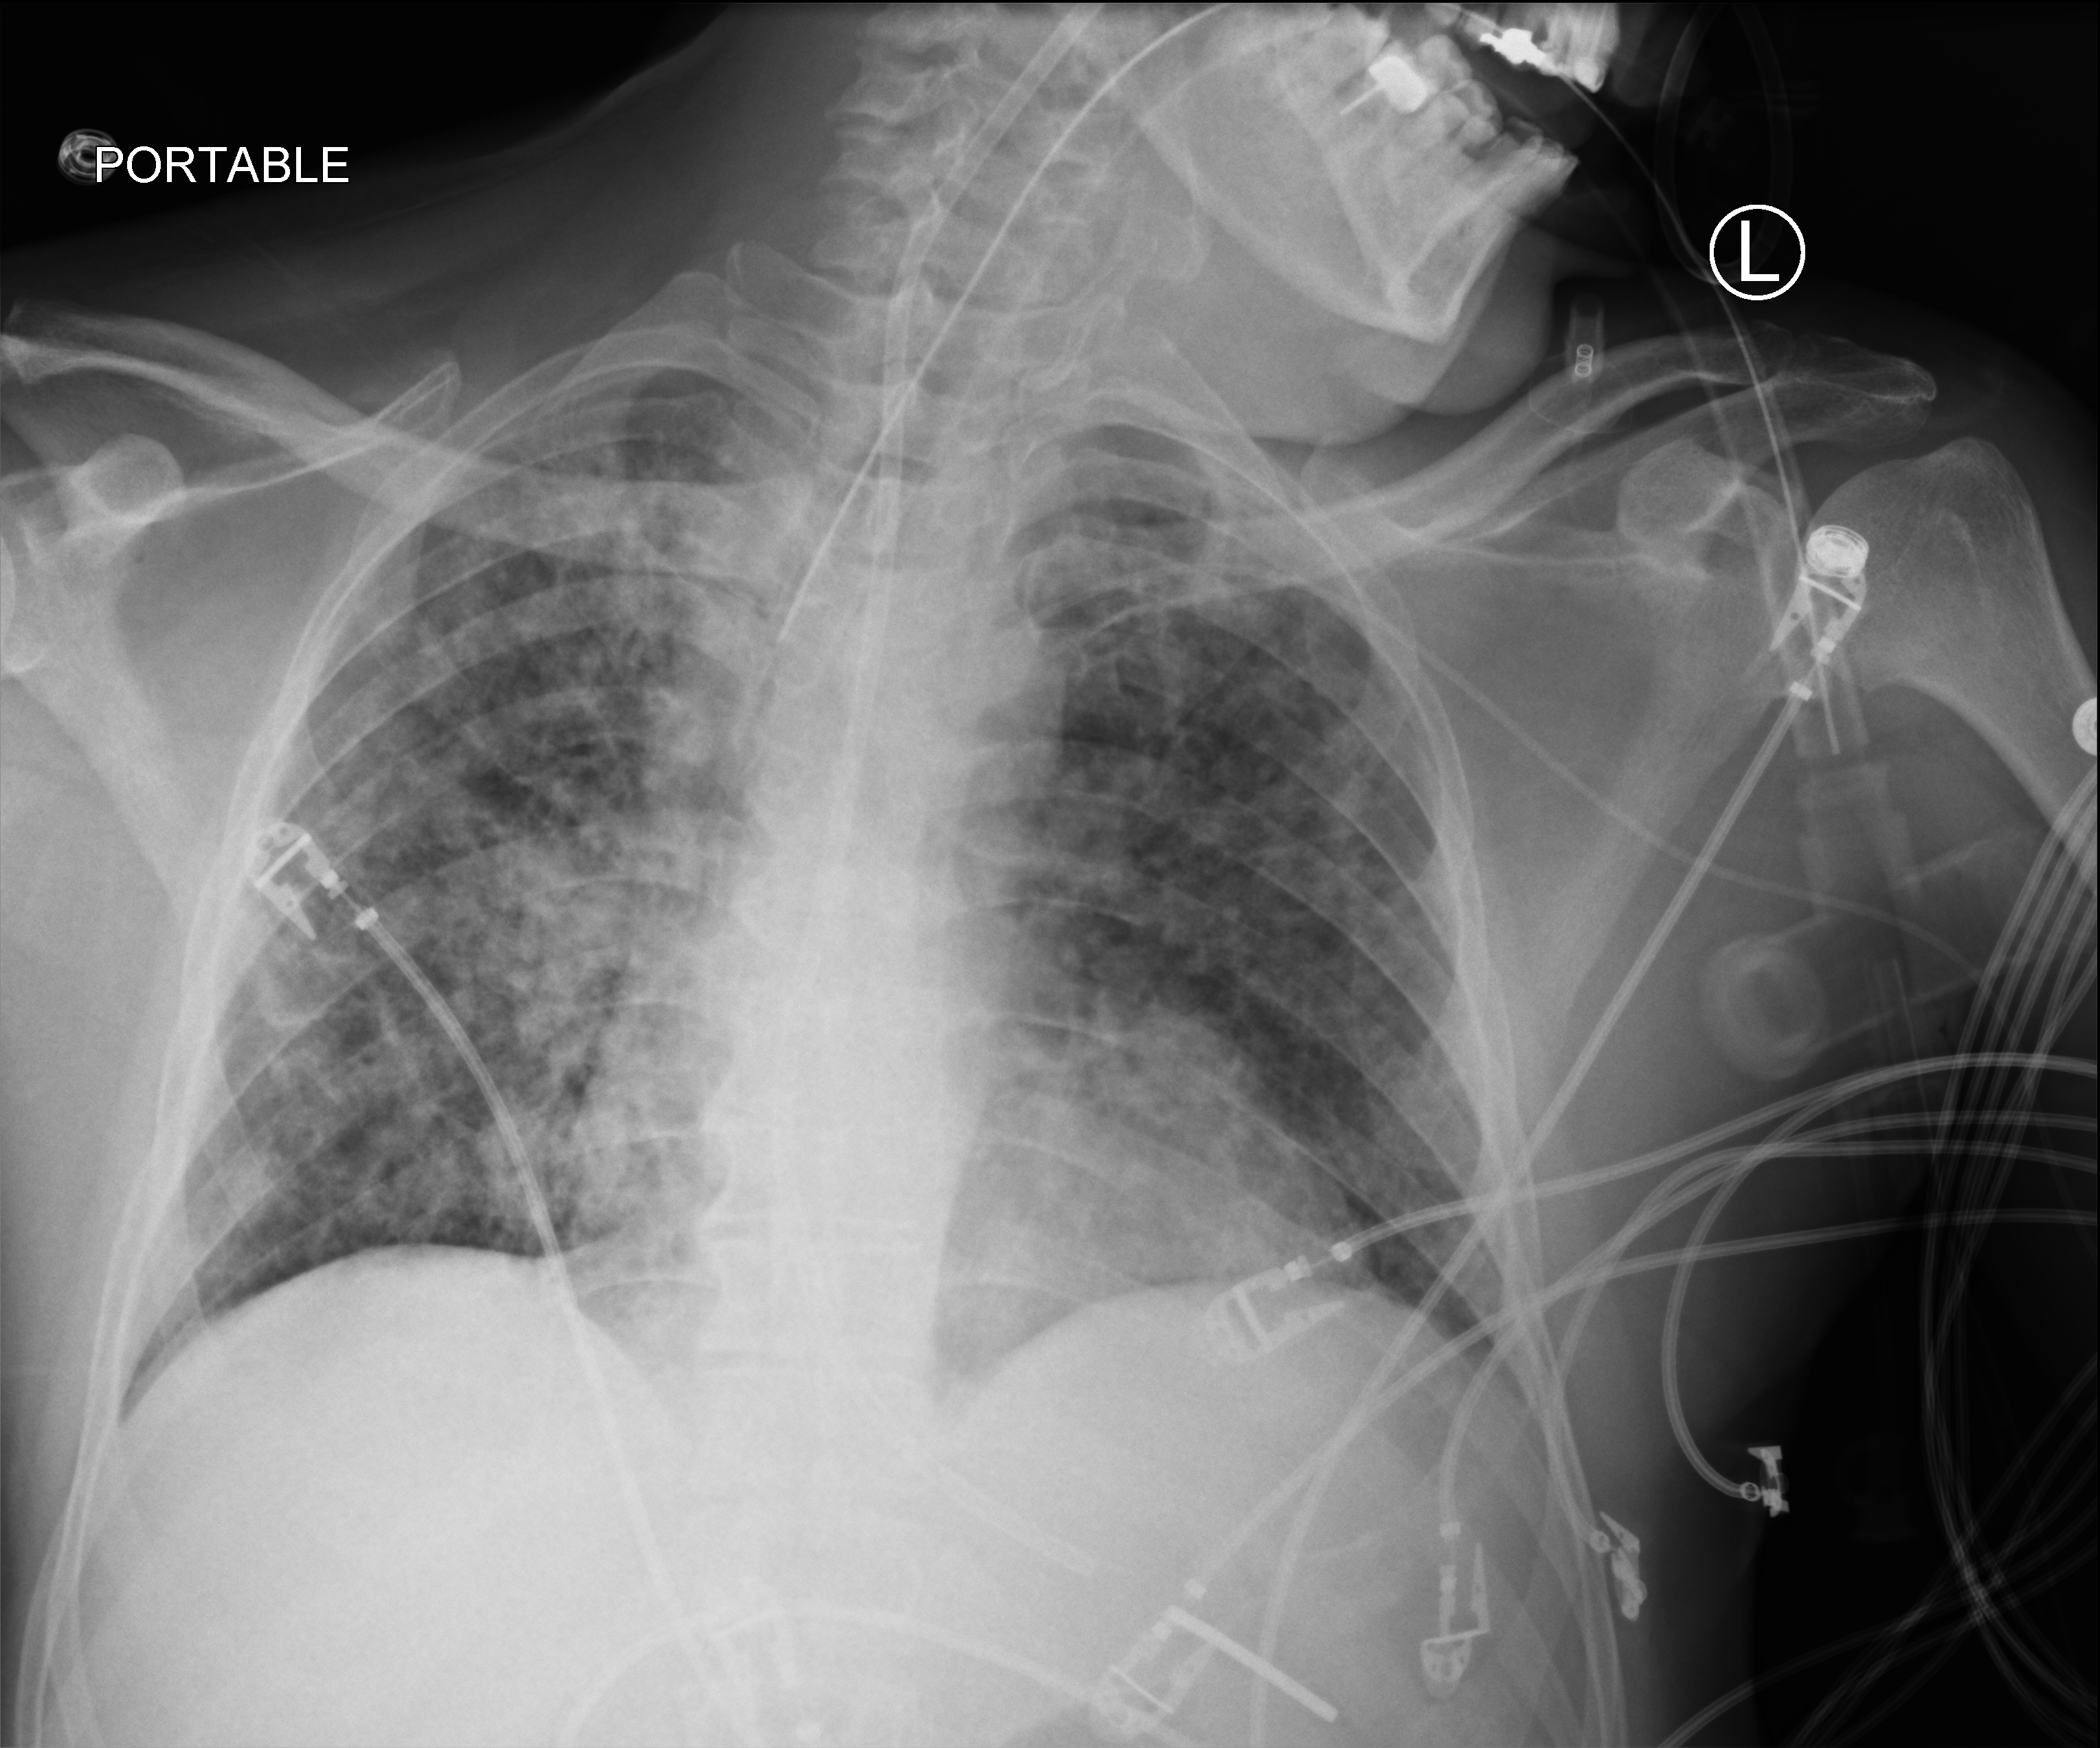
Portable chest radiograph, anteroposterior (AP) projection. Male patient hospitalised with COVID-19, age 18–59 years.
From the hospital-stay record, not from the radiograph (when in the stay this image was taken is not recorded): admitted to intensive care during this hospital stay: yes.